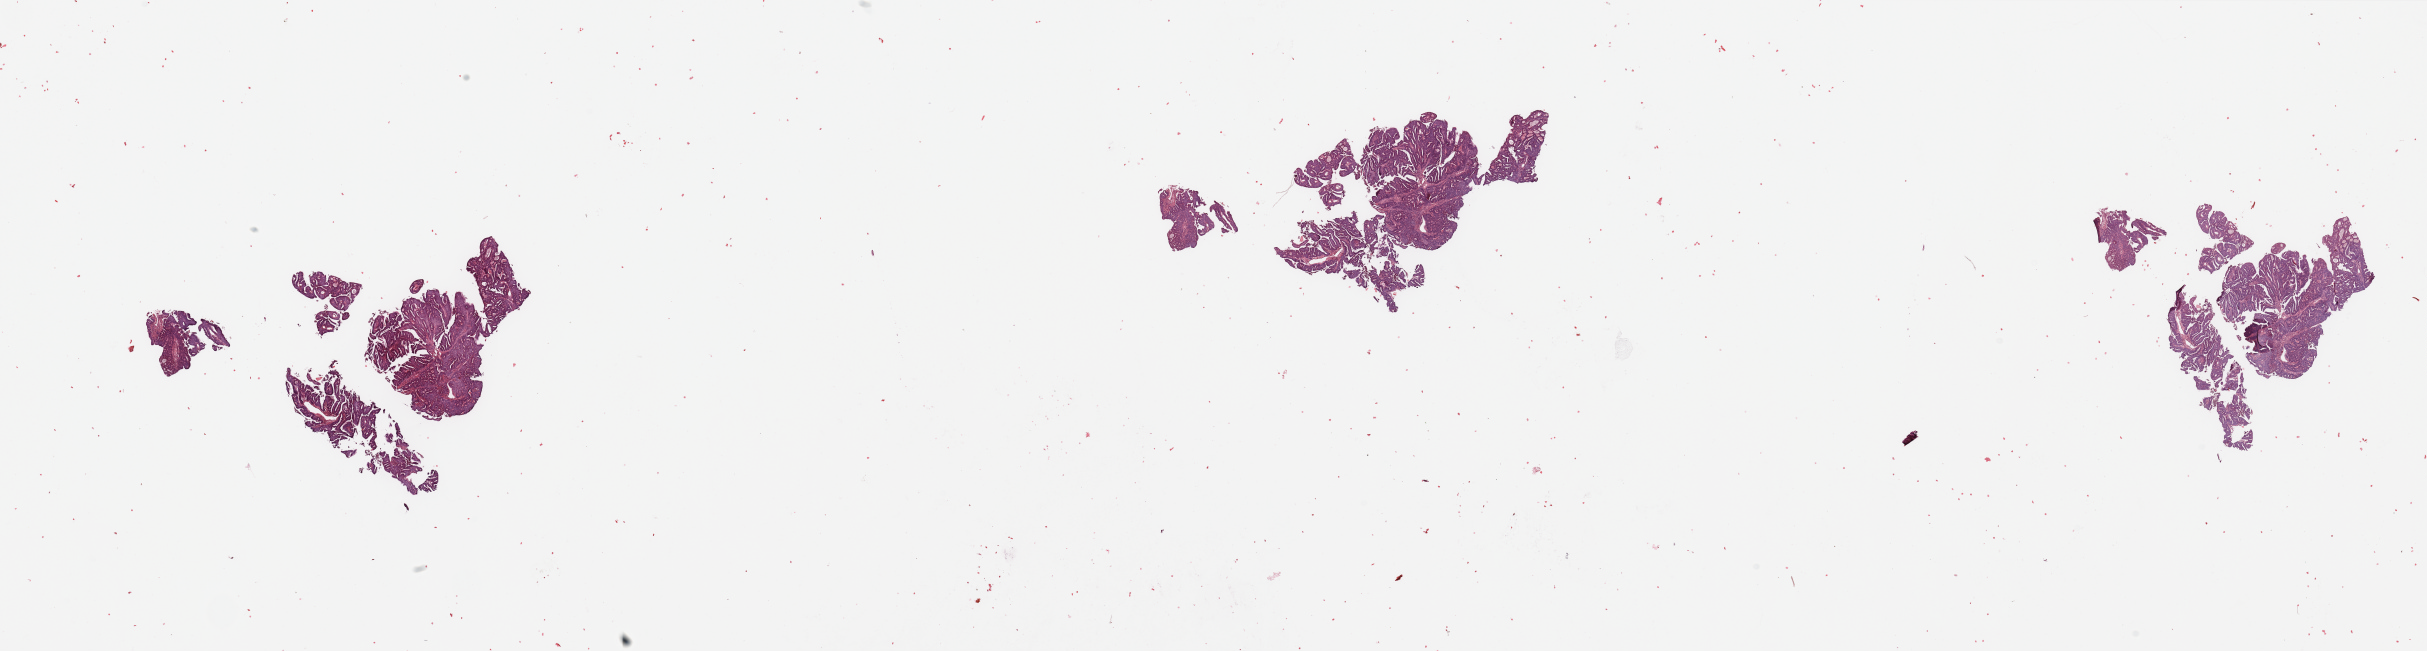
Digitized Hematoxylin and eosin (H&E) stained tissue section (whole slide) — shown as a low-resolution overview of the whole scanned area (about 38.4 x 10.3 mm), tumour tissue sample, uterus. Female, 69 y/o.
* patient diagnosis (cohort enrolment): corpus endometrial carcinoma (uterus)
* primary tumour site (as recorded): anterior endometrium